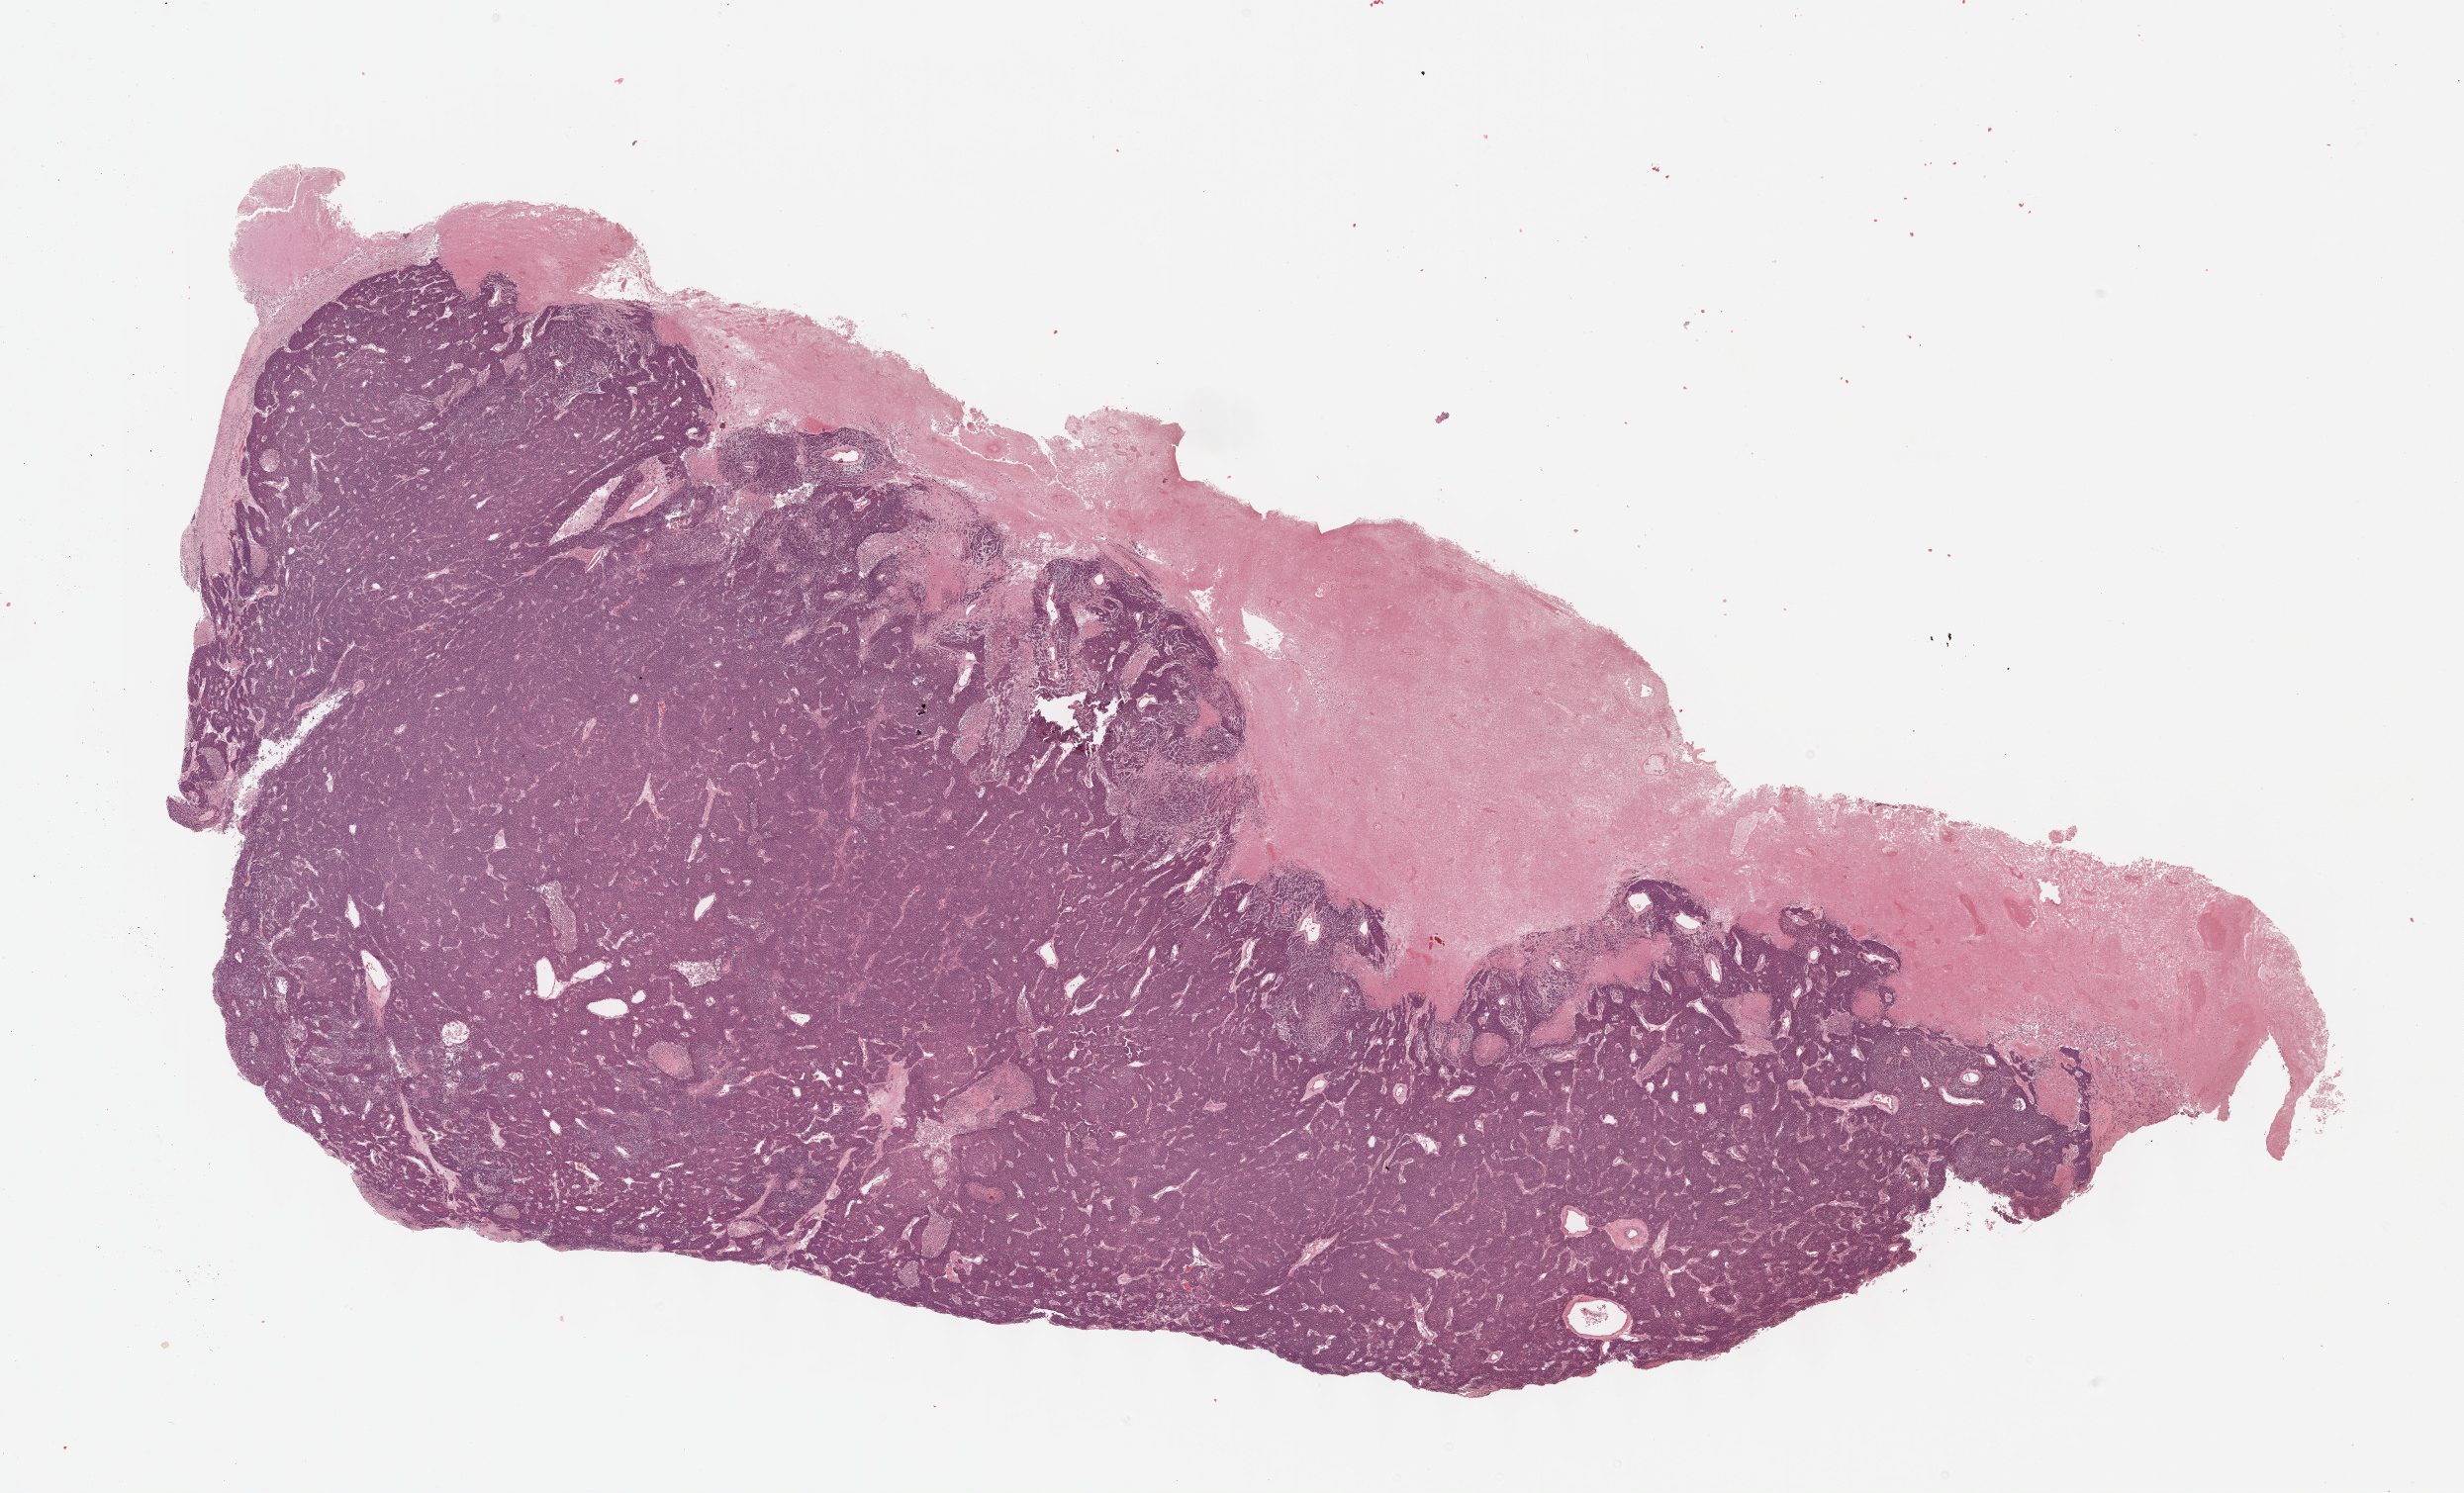
Digitized H&E tissue section (whole slide) — whole scanned area (about 20.1 x 12.2 mm) shown as a low-resolution overview; formalin-fixed paraffin-embedded (FFPE) diagnostic section; uterus, primary tumour sample. Female, age 66 years at initial diagnosis.
Histologic diagnosis: Endometrioid adenocarcinoma, NOS (endometrium).